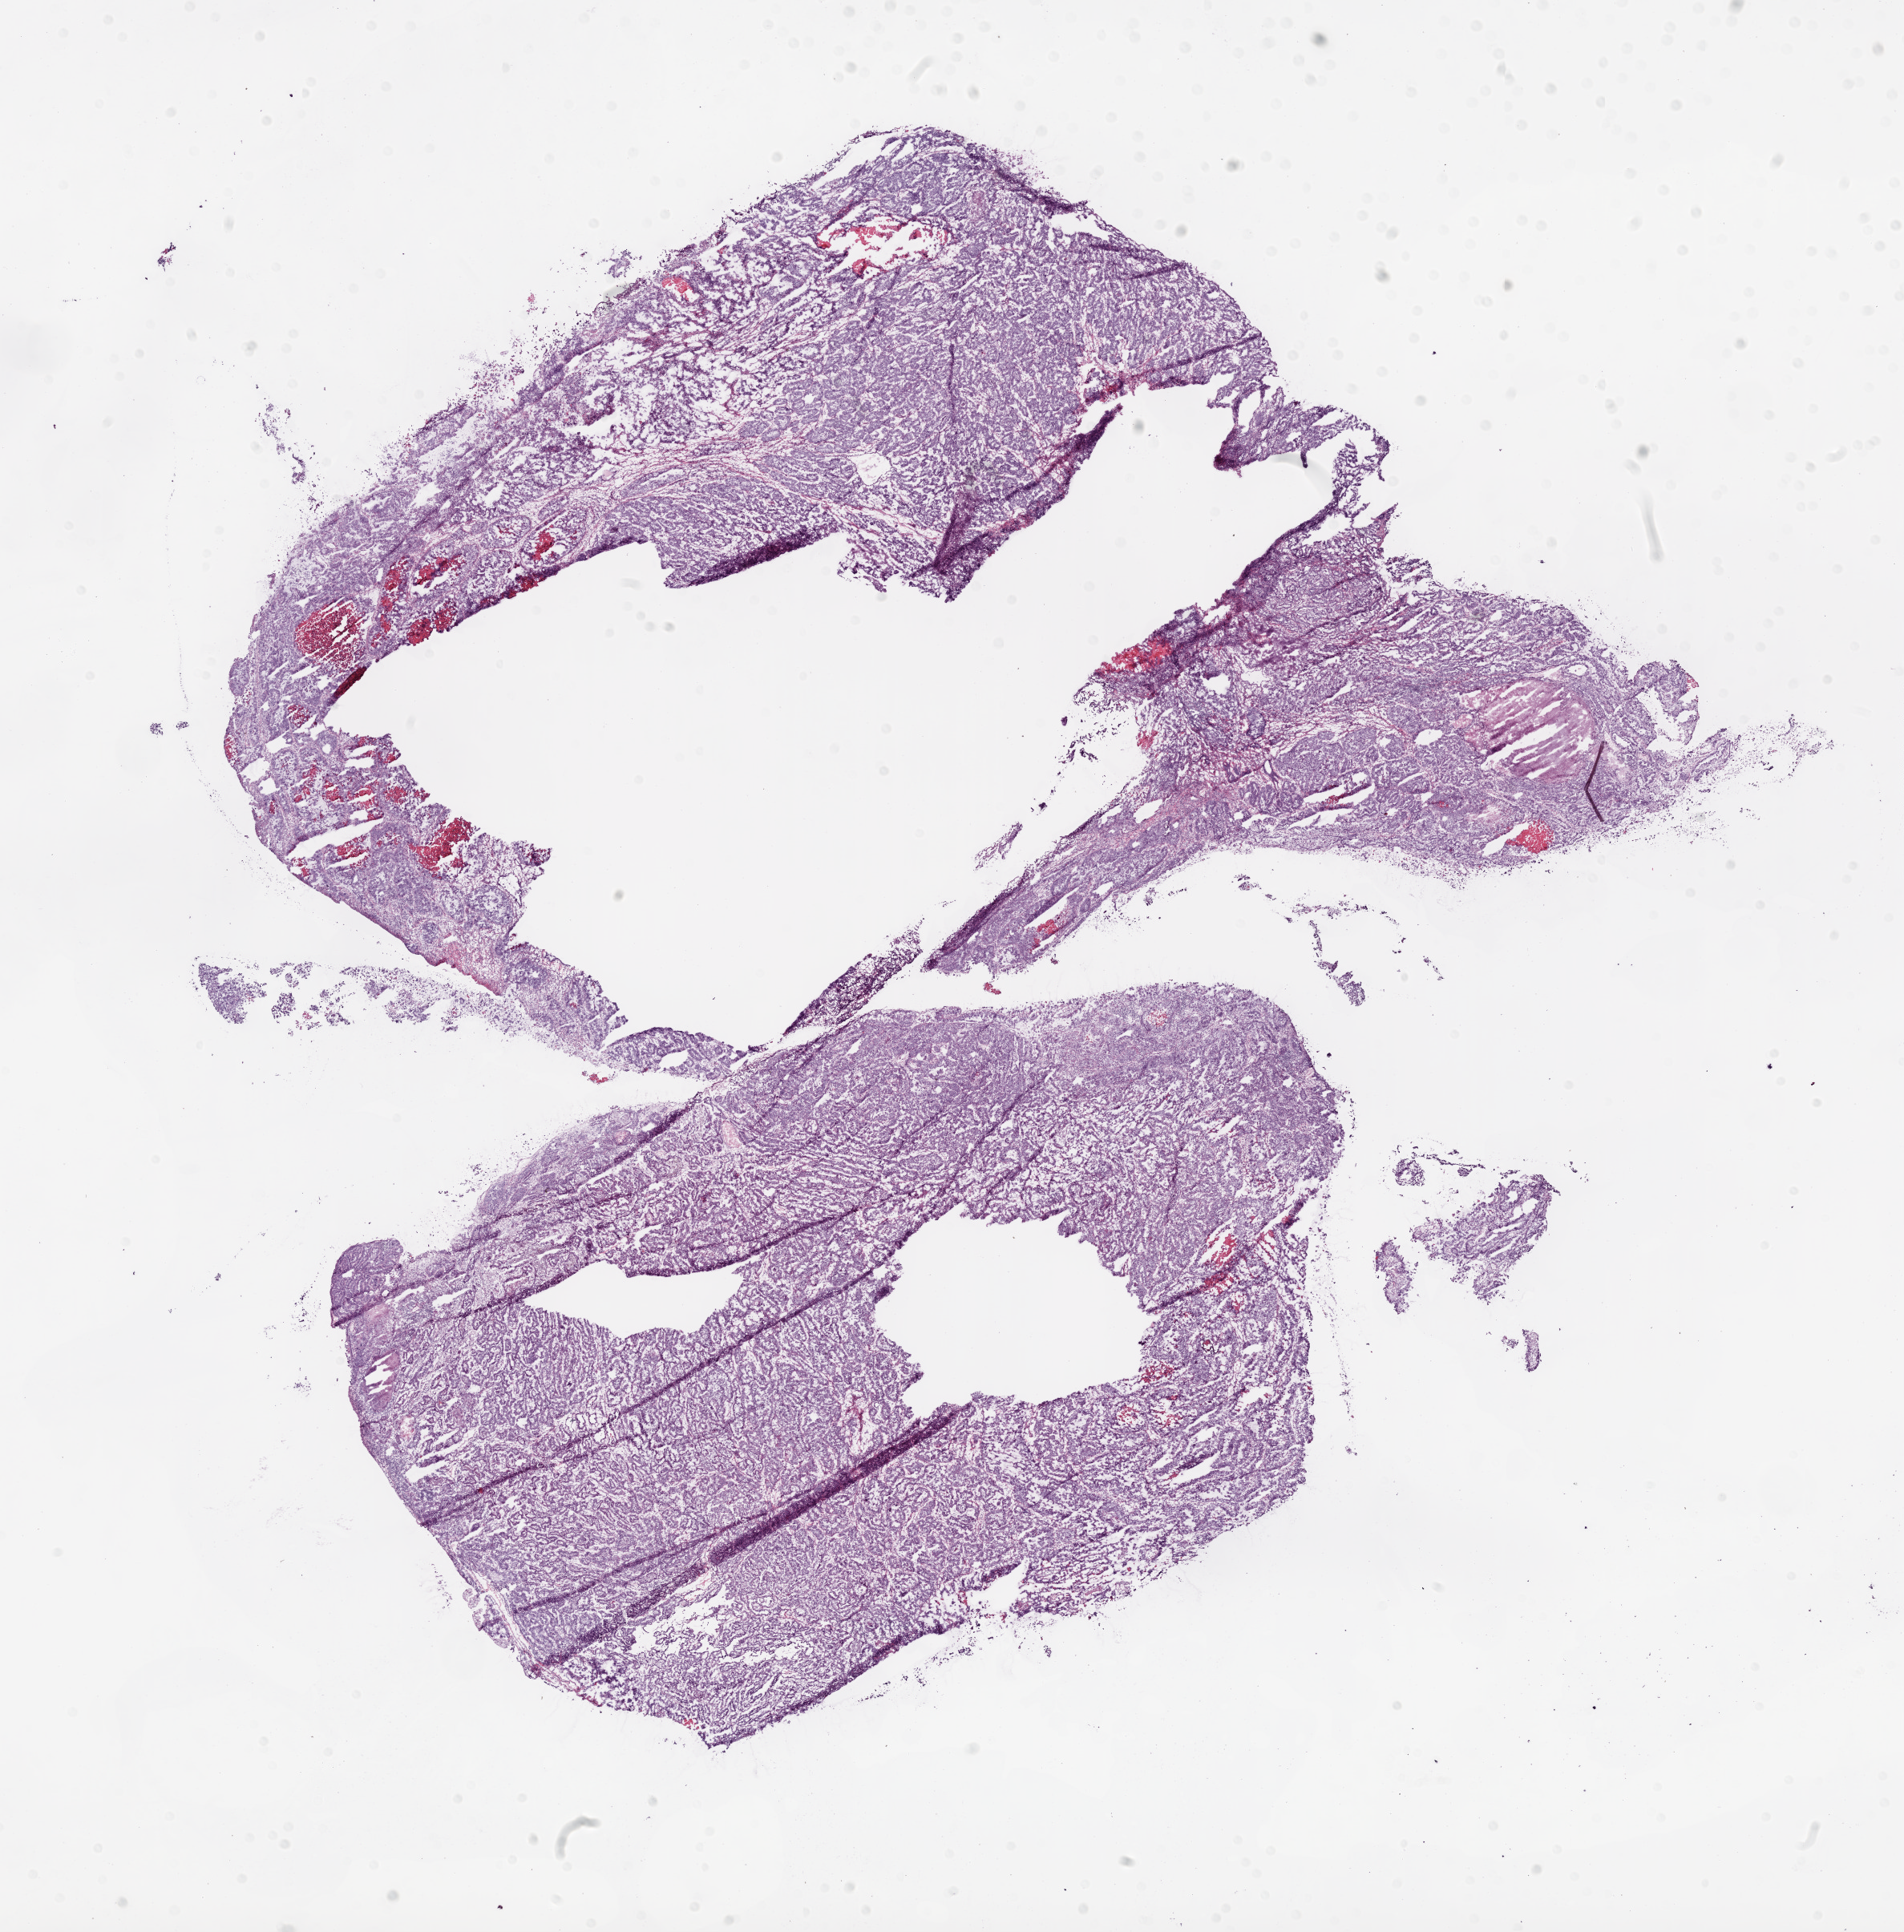
Hematoxylin and eosin (H&E) stained whole-slide image — a low-resolution overview of the entire scanned area, about 19.1 x 19.3 mm. Frozen section from the bottom of the tissue portion. Ovary, primary tumour sample. Female patient; age at initial diagnosis 61 years. Histologic grade: G3 (poorly differentiated). Pathologist review of this section (percent, as recorded): tumour cells 85%, tumour nuclei 80%, normal cells 0%, stromal cells 5%, necrosis 10%.
Histologic diagnosis: Serous cystadenocarcinoma, NOS. FIGO stage: IV. Laterality: left.